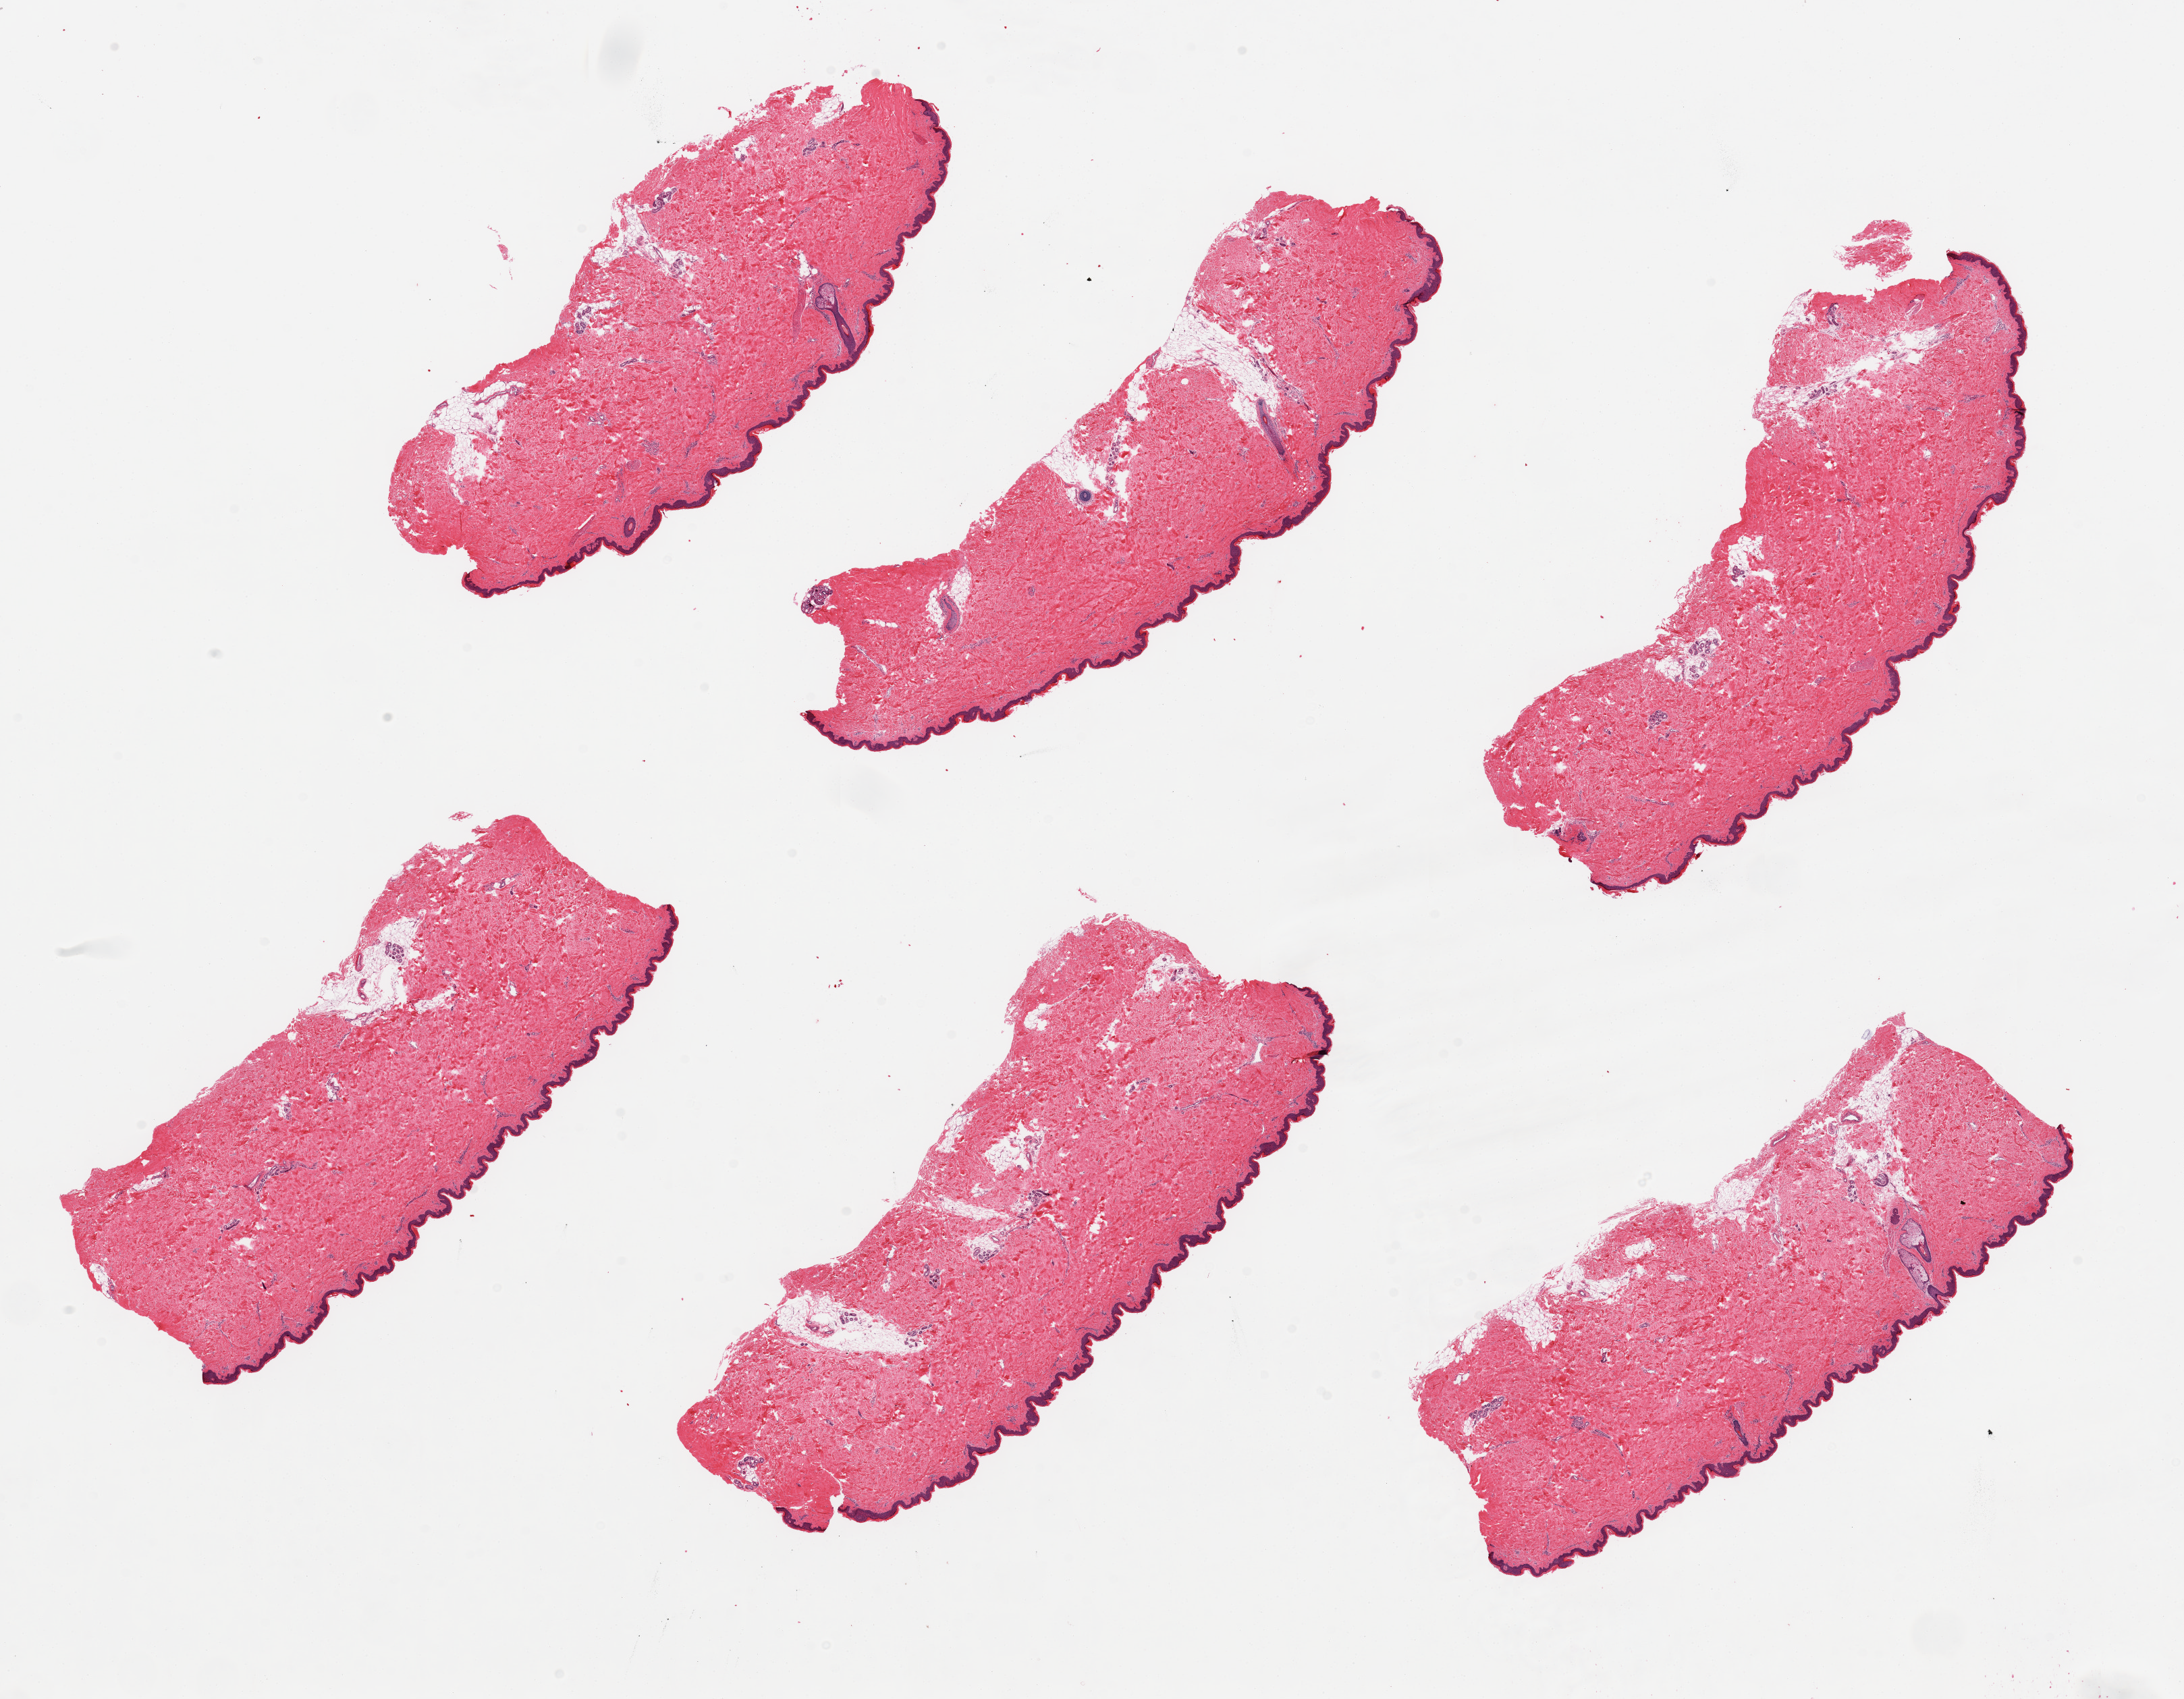
Digitized haematoxylin and eosin-stained section, brightfield, whole scanned area (about 25.6 x 19.9 mm) shown as a low-resolution overview, PAXgene-fixed paraffin-embedded (PFPE) section, sampled site (target tissue): skin of lower leg, donor tissue sample. Donor: female.
• pathologist's review note for this sample: 6 pieces, well trimmed with minimal internal adipose tissue, squamous epithelium measures 40-70 microns